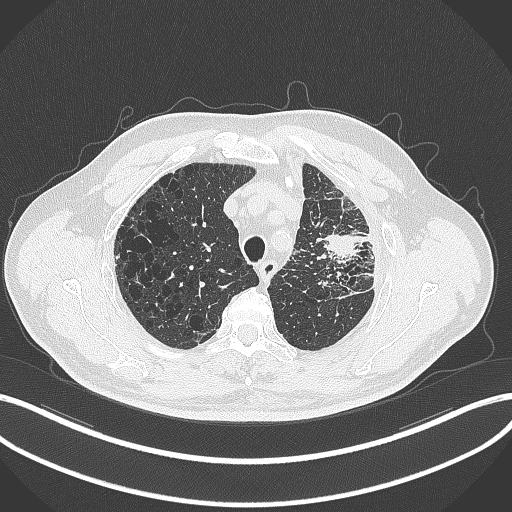
Chest CT, one axial slice. Position 258 of 297 along the scan axis. Reconstruction kernel B70f. Lung window (W 1500 / L -600 HU). 512 × 512 image matrix, field of view 400 × 400 mm. Male patient, age 68 years. From the clinical record (not read from this slice): clinical TNM (as recorded): T3 N3 M1.
Annotated regions visible in this slice (rectangle marked by the reading radiologist):
- lung tumour (recorded histology: adenocarcinoma): bounding box <319,224,363,267> (left, top, right, bottom; pixels)